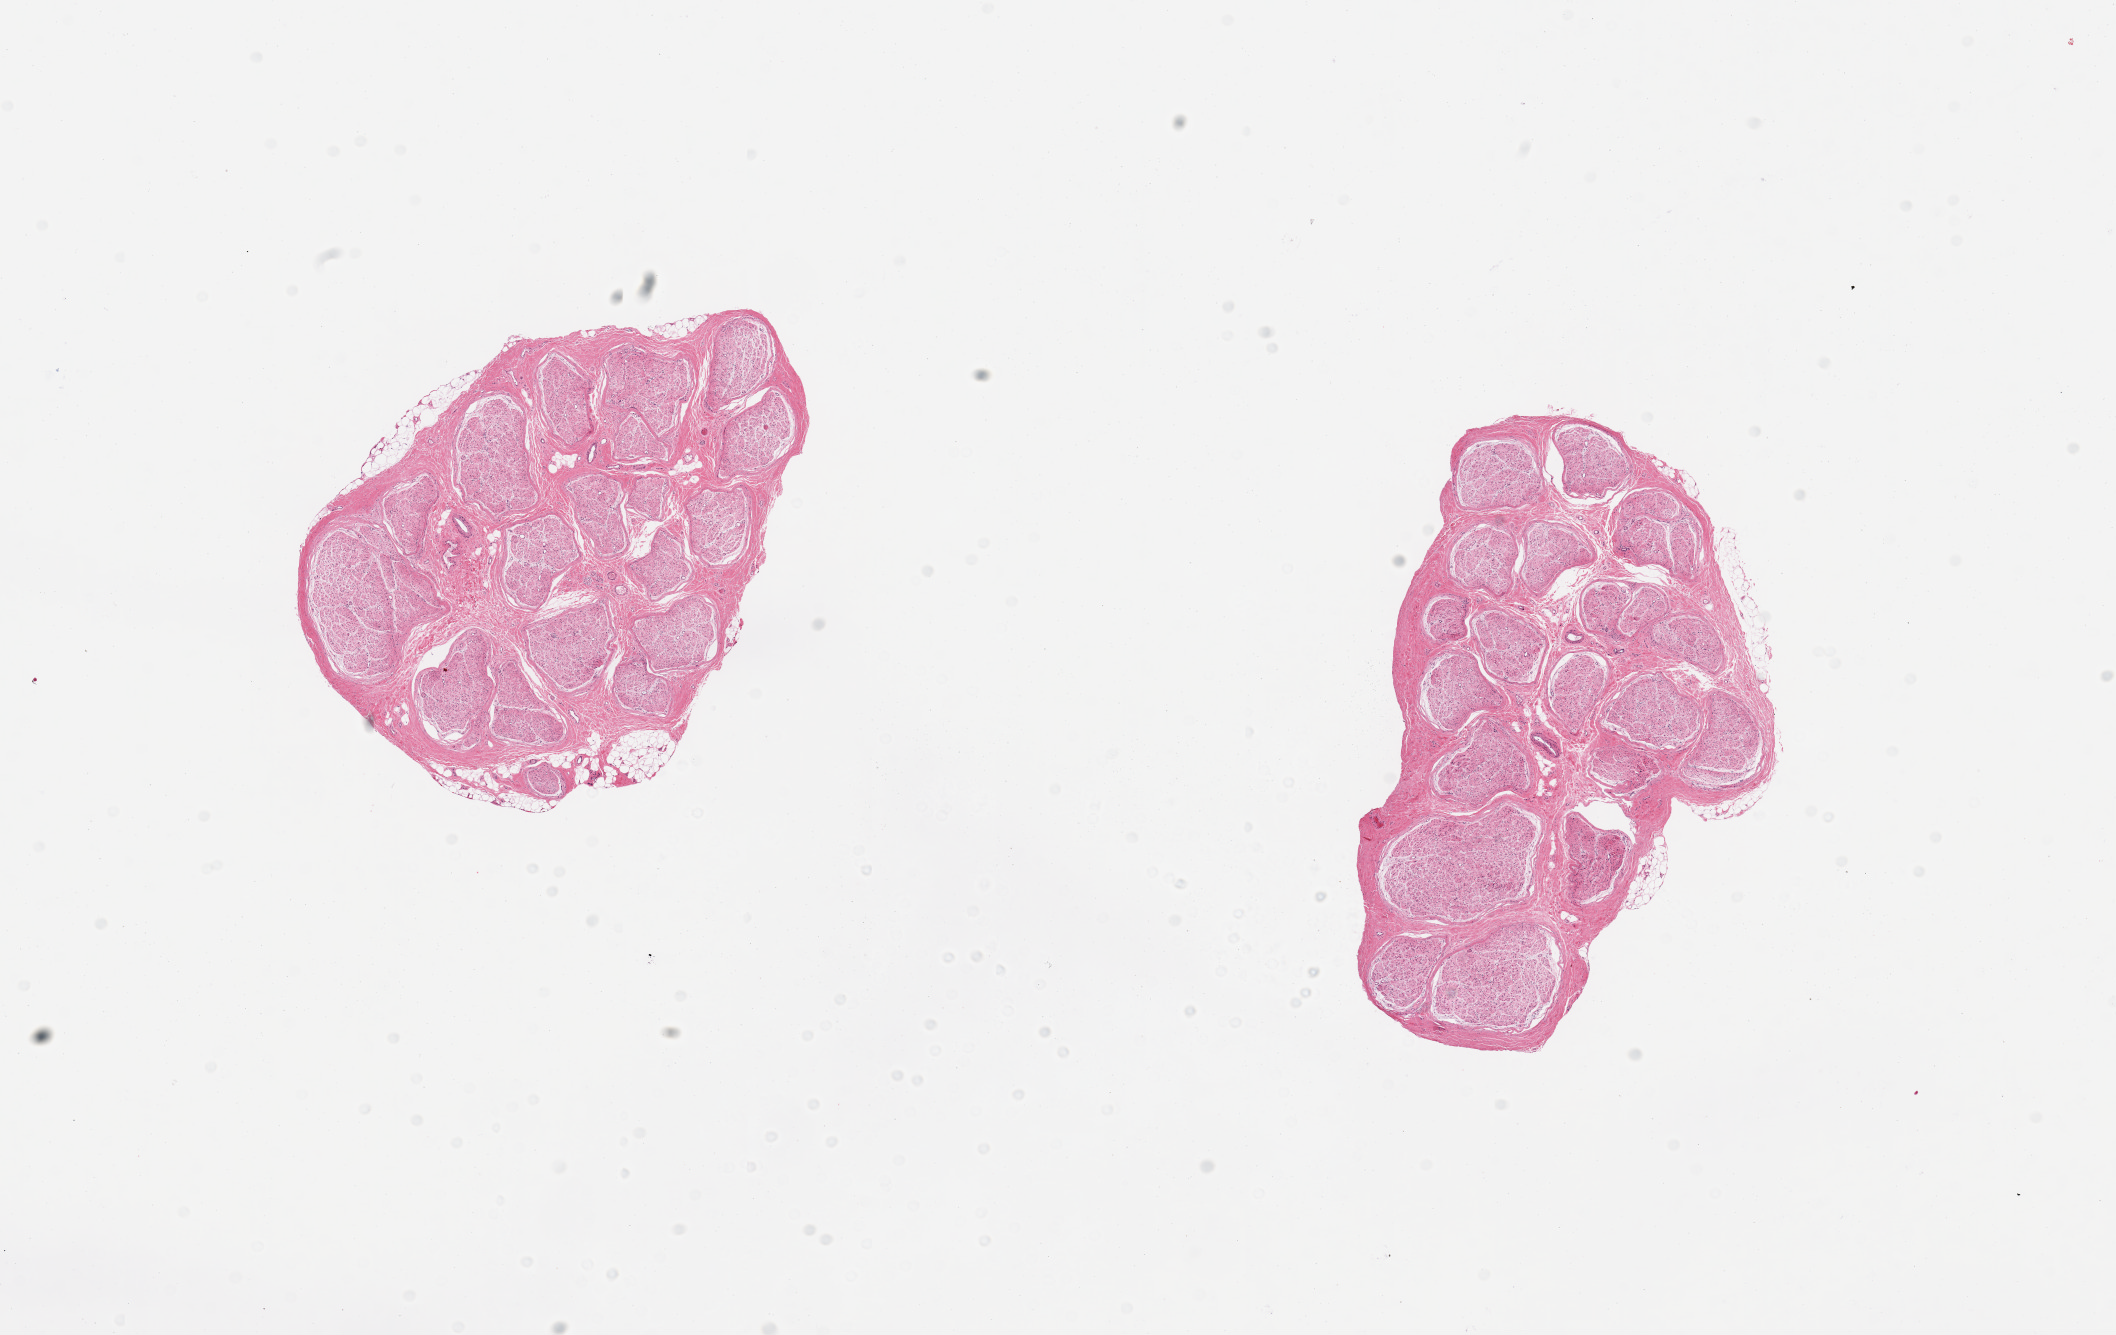
Whole-slide image, hematoxylin and eosin (H&E) stain — whole scanned area (about 16.7 x 10.6 mm) shown as a low-resolution overview. PAXgene-fixed paraffin-embedded (PFPE) section. Section of tibial nerve (target tissue). Tissue donor sample. Male donor.
Pathologist's review note for this sample: 2 pieces; rim of external fat.